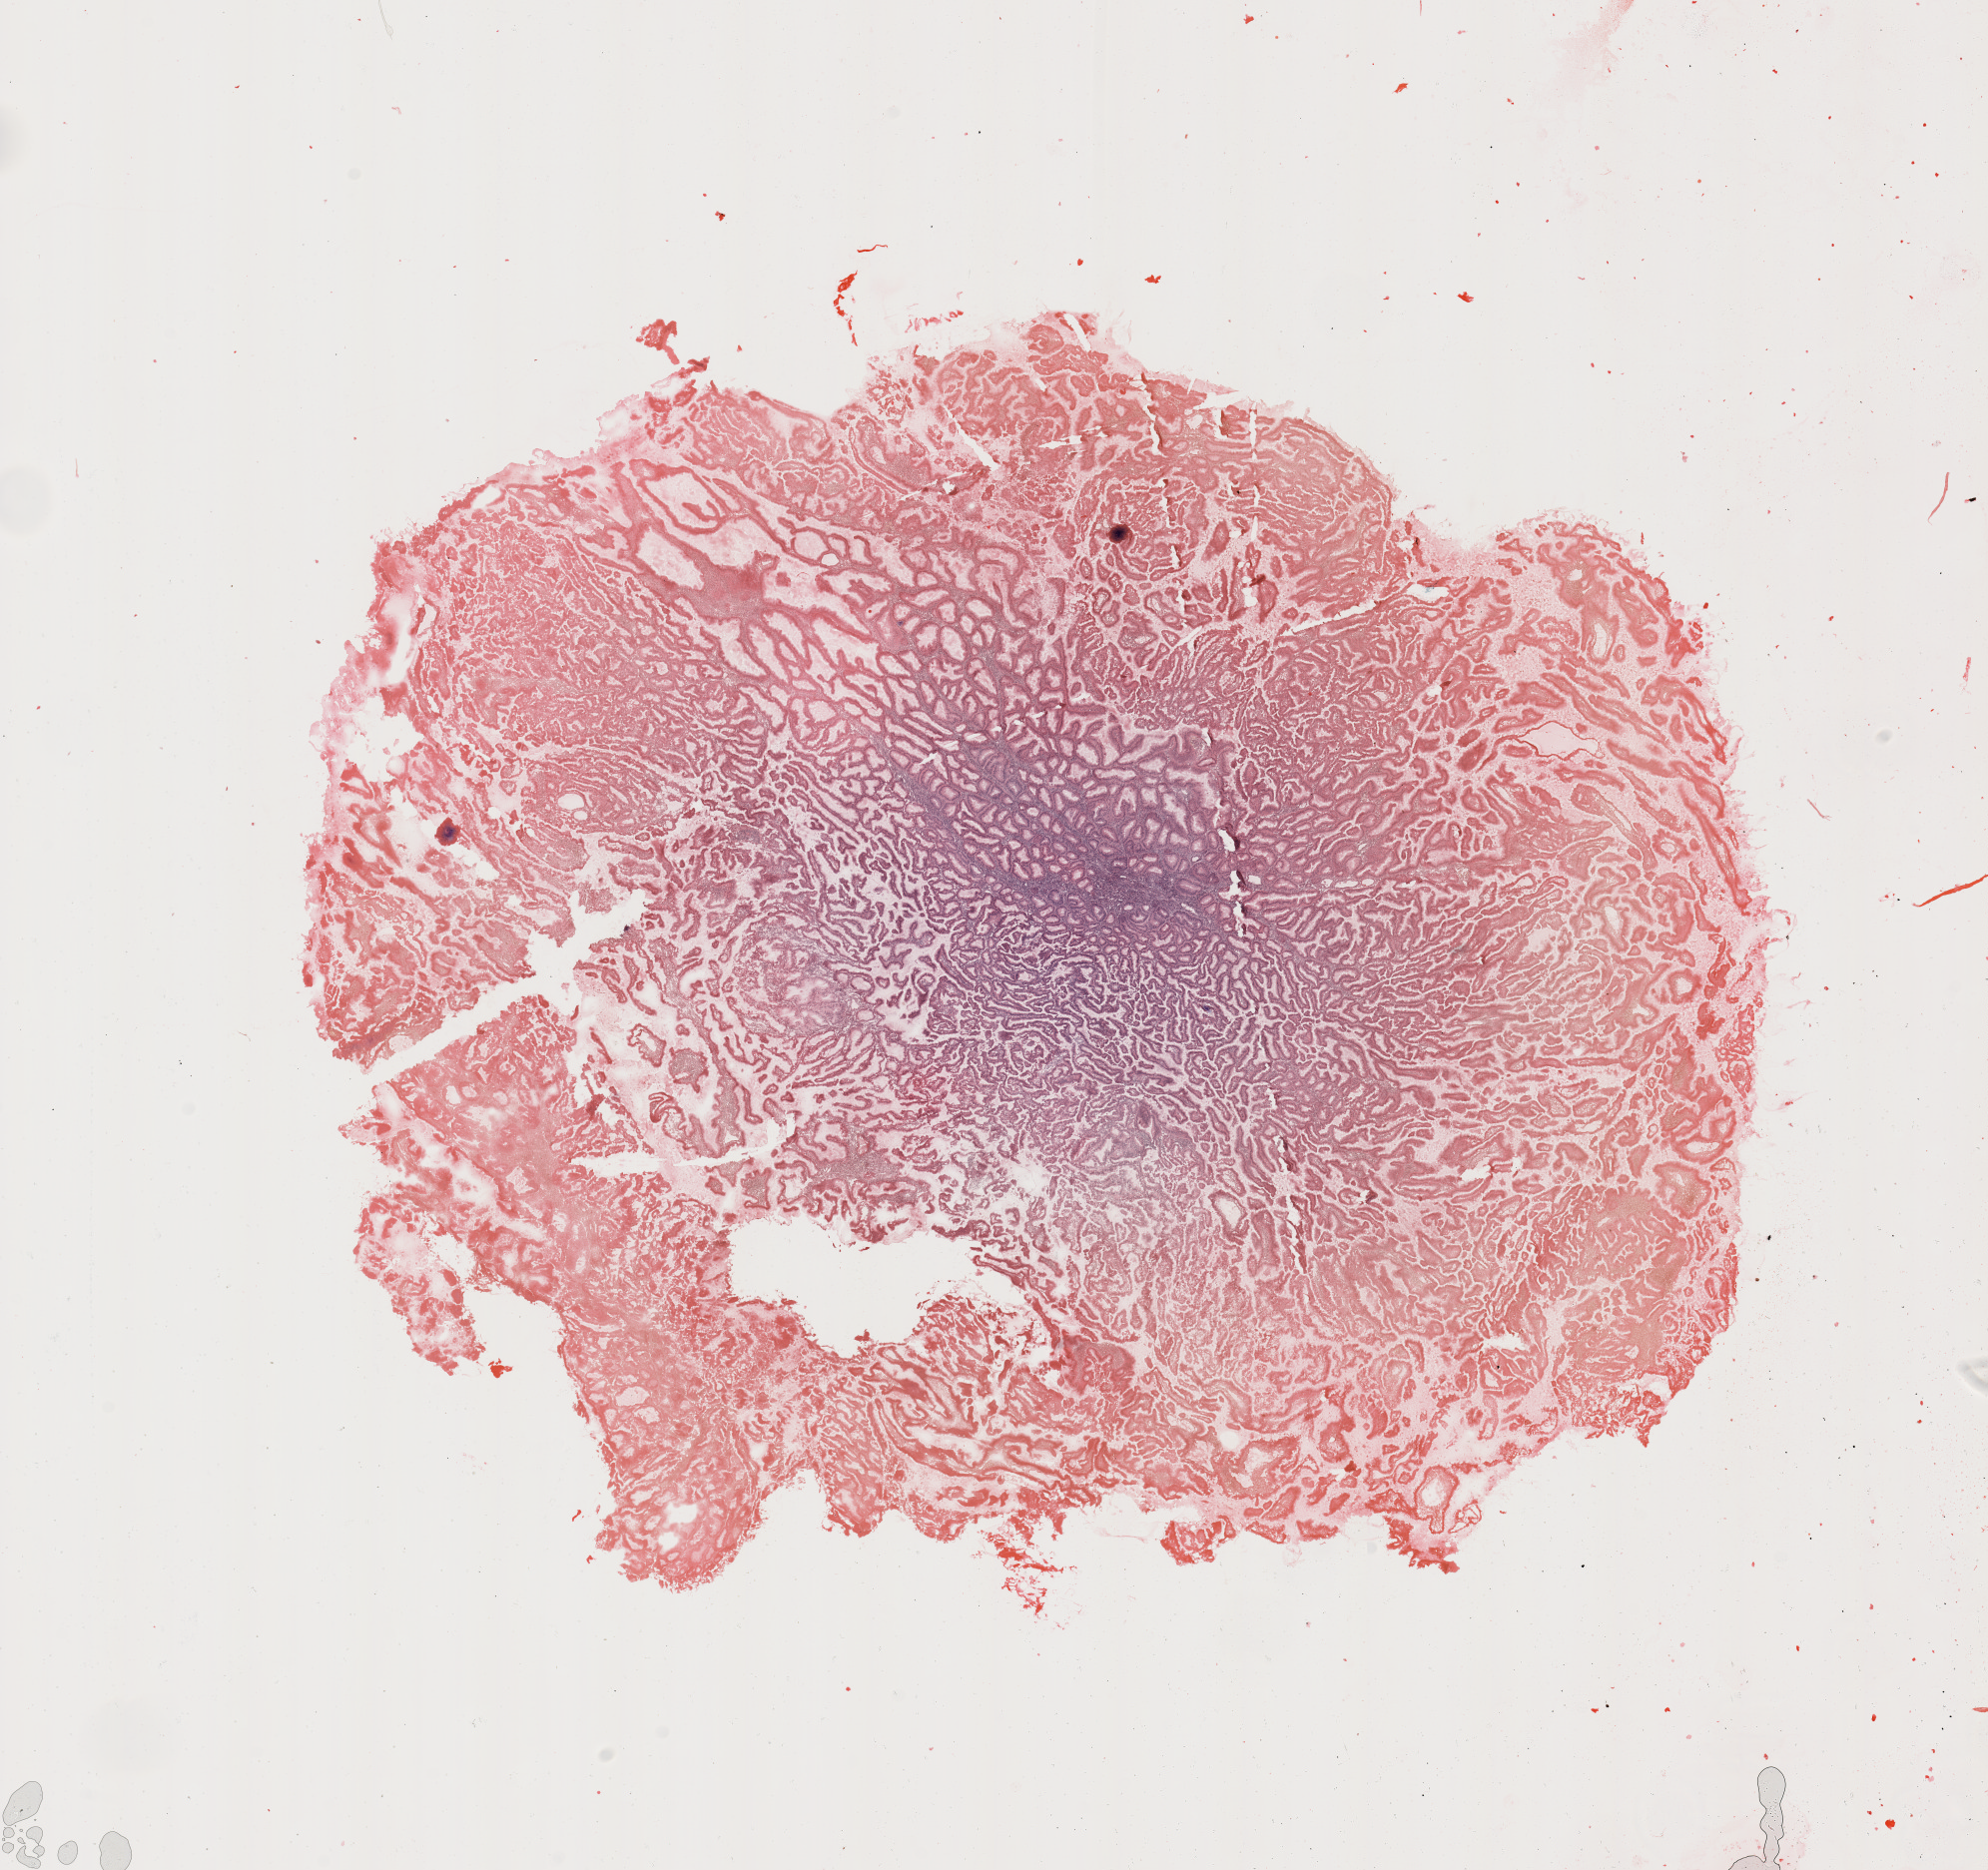
Digitized H&E tissue section (whole slide), shown as a low-resolution overview of the whole scanned area (about 15.8 x 14.8 mm, from a 20x scan). Tumour tissue sample, uterus. Female, 61 y/o. Histologic grade: G1 (well differentiated).
Histologic diagnosis: Endometrioid adenocarcinoma, NOS. AJCC pathologic stage: I.